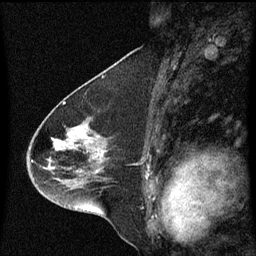
Breast MRI (dynamic contrast-enhanced), one sagittal slice. Slice 35 of 60 in the series (ordered by position). Dynamic contrast-enhanced series, image 2 of 3 at this slice position (ordered by acquisition). 1.5 T. TE 4.2 ms, TR 8.4 ms. 2 mm slice thickness. 256 × 256 image matrix, field of view 200 × 200 mm. Patient: female, 46 years. From the clinical record (not read from this slice): setting: breast cancer imaged before/during neoadjuvant chemotherapy; receptor status: HER2-positive.
Annotated regions visible in this slice (semi-automatic segmentation, software-assisted and operator-edited):
- analysis volume of interest (the breast-tissue region the enhancement analysis was run in; not a lesion): bounding box <27,112,148,195> (left, top, right, bottom; pixels)
- tumour enhancement mask (voxels above the 70 % enhancement threshold inside the analysis volume of interest): <57,140,63,143>